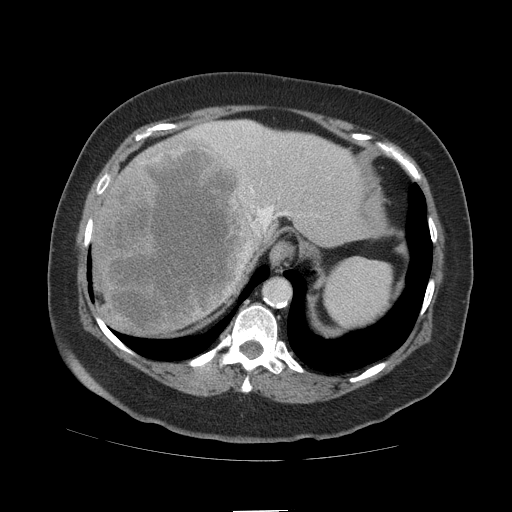
Contrast-enhanced abdominal CT (liver protocol), one axial slice; position 86 of 109 along the scan axis; reconstruction kernel STANDARD; soft-tissue window (W 400 / L 40 HU); 2.5 mm slice thickness; 512 × 512 image matrix, field of view 420 × 420 mm. From the clinical record (not read from this slice): diagnosis: hepatocellular carcinoma (patient treated with transarterial chemoembolisation; whether this scan precedes or follows treatment is not stated here); TNM stage (as recorded): Stage-IVB; Child-Pugh class: A.
Annotated regions visible in this slice (semi-automatically segmented with operator editing):
- abdominal aorta: bounding box (x1, y1, x2, y2) in pixels: (265, 280, 290, 303)
- liver parenchyma outside the tumour (the mass and vessels are separate outlines, so this box may not span the whole liver): (92, 120, 382, 334)
- mass: (94, 138, 259, 333)
- liver vessels: (196, 122, 288, 267)